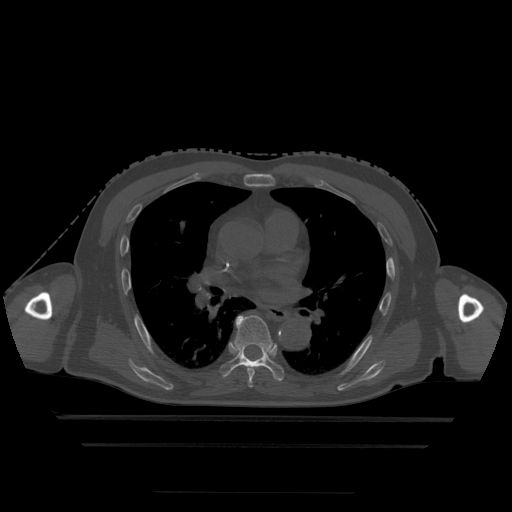
CT including the spine, one axial slice. Slice 304 of 522 in the series (ordered by position). Bone window (W 1800 / L 400 HU). 1.25 mm slice thickness. 512 × 512 image matrix, field of view 436 × 436 mm. Patient age 68 years. From the clinical record (not read from this slice): primary cancer: urothelial.
Annotated regions visible in this slice (semi-automatic segmentation, software-assisted and operator-edited):
- T5 vertebra: bounding box [x1, y1, x2, y2] px = [248, 379, 253, 388]
- T6 vertebra: [247, 368, 255, 380]
- T7 vertebra: [220, 316, 284, 382]